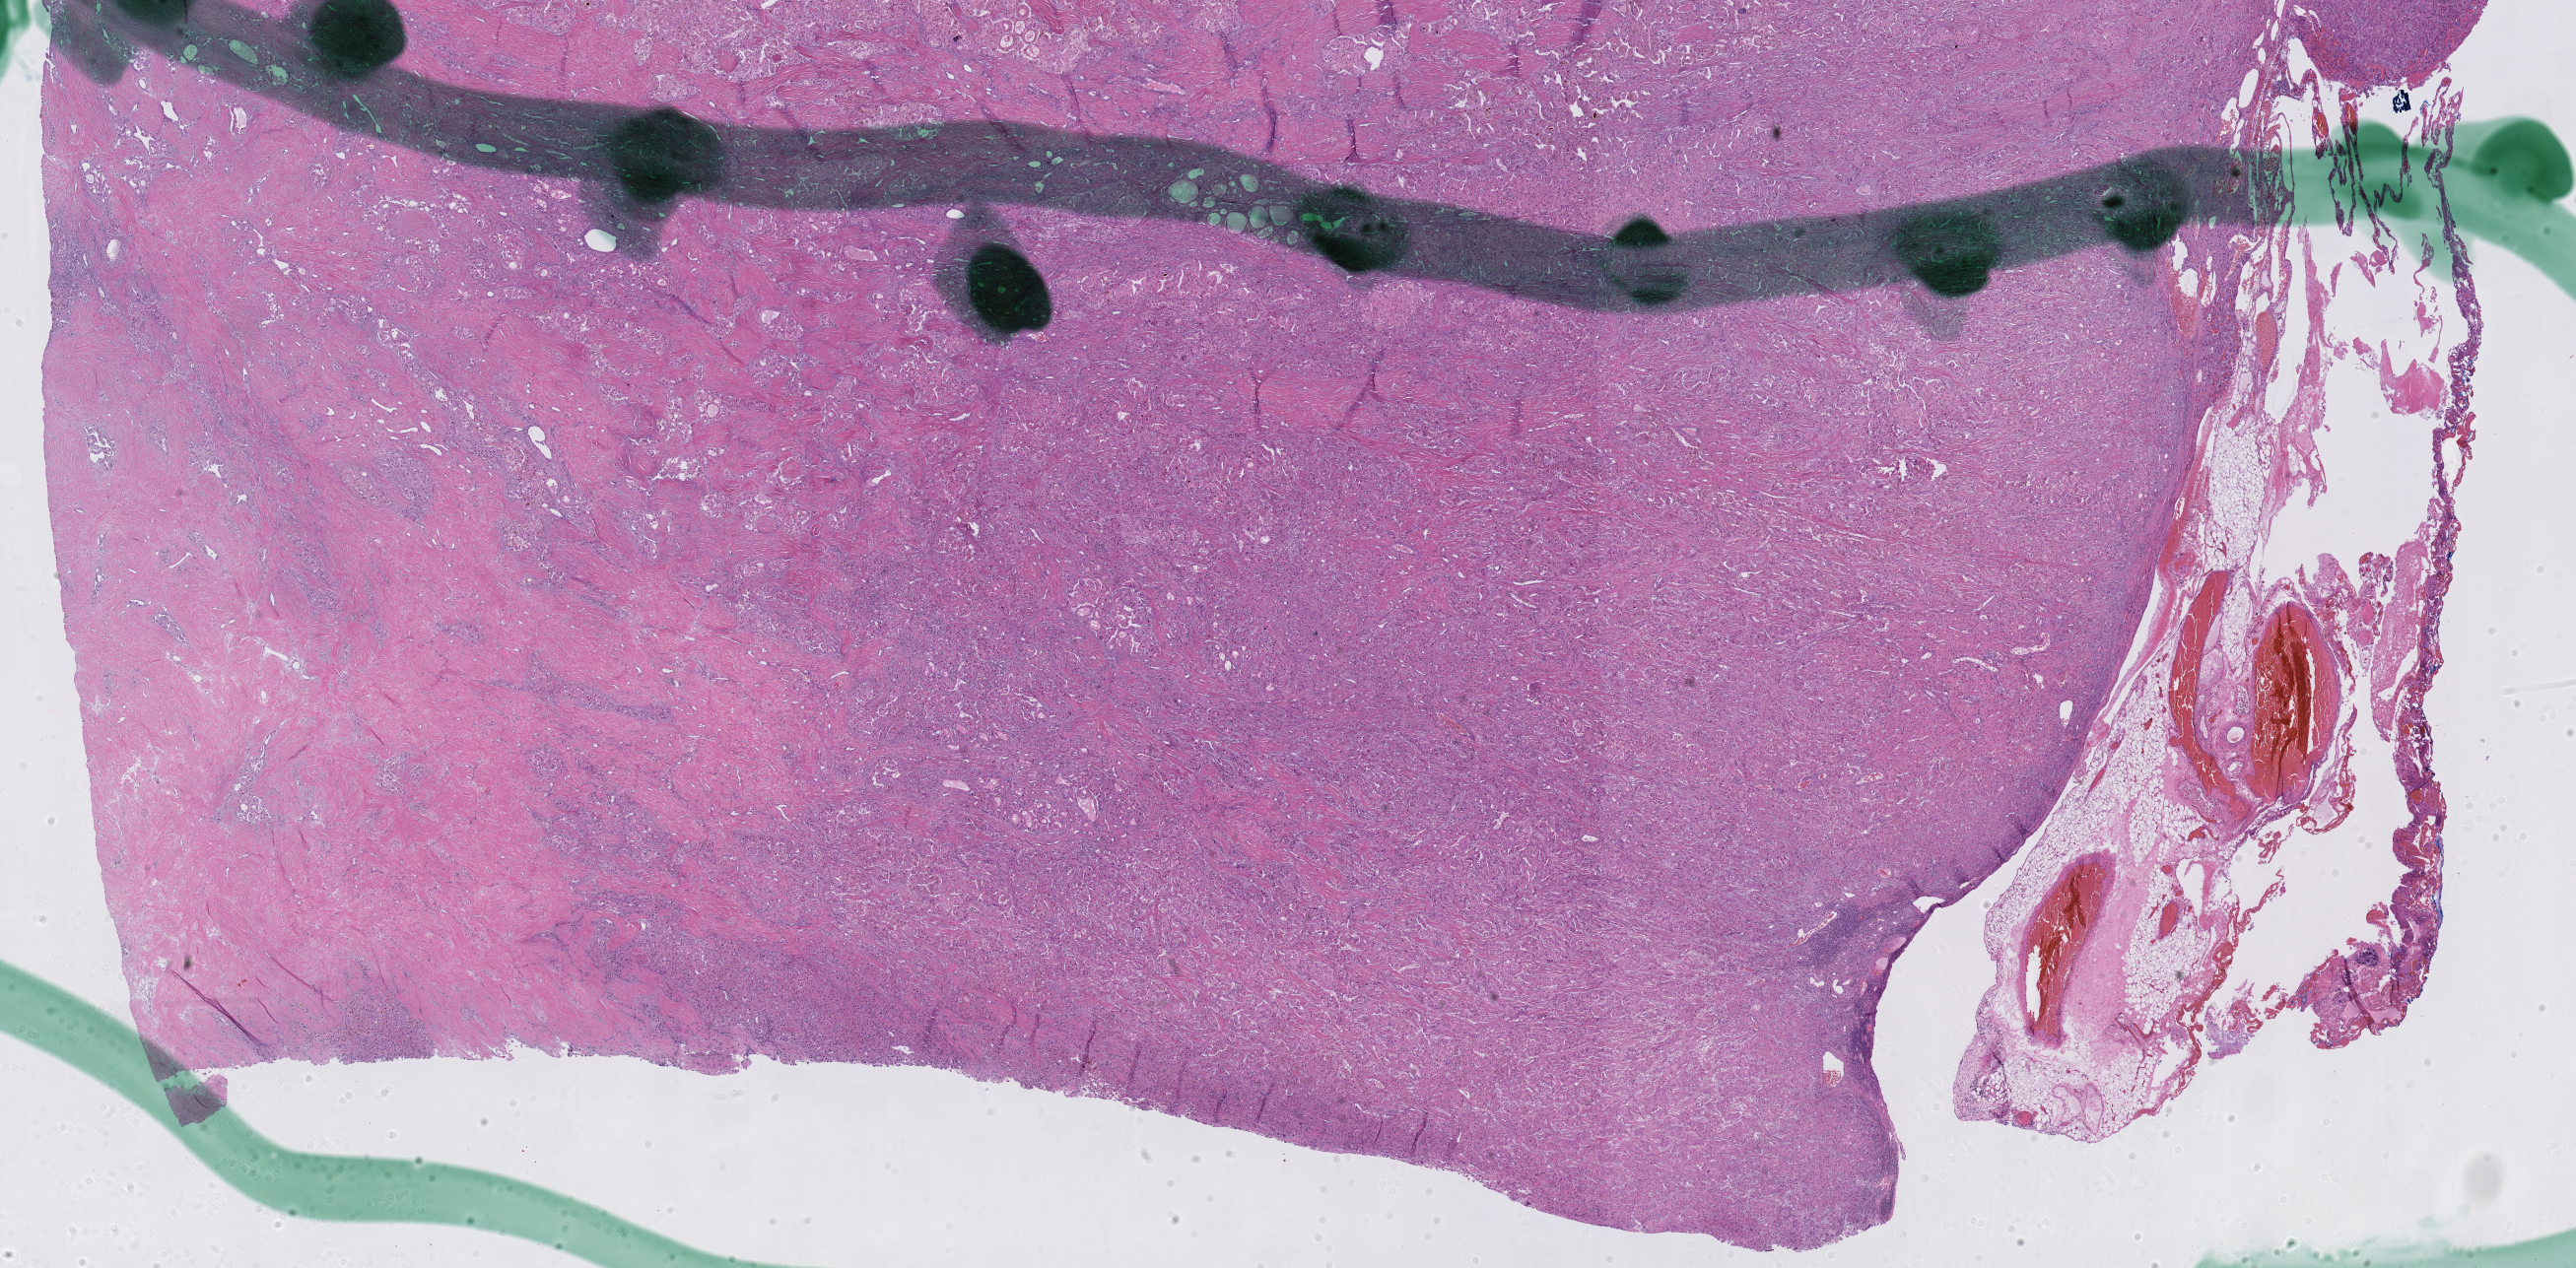
Digitized H&E tissue section (whole slide), low-resolution overview of the scanned area, about 21.2 x 10.4 mm (from a 40x scan), FFPE section, liver, primary tumour sample. Patient: female, age at initial diagnosis 20 years. Histologic grade: G2 (moderately differentiated).
* diagnosis: Hepatocellular carcinoma, fibrolamellar
* AJCC pathologic stage: IVA (7th edition)